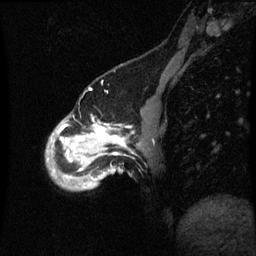
Breast MRI (dynamic contrast-enhanced), one sagittal slice. Position 14 of 60 along the scan axis. Dynamic contrast-enhanced series, image 2 of 3 at this slice position (ordered by acquisition). 1.5 T. TE 4.2 ms, TR 8.9 ms. 2 mm slice thickness. 256 × 256 image matrix, field of view 200 × 200 mm. Female patient, age 49 years. From the clinical record (not read from this slice): setting: breast cancer imaged before/during neoadjuvant chemotherapy; receptor status: HR-positive, HER2-negative.
Structures marked on this image (semi-automatic segmentation, software-assisted and operator-edited):
- analysis volume of interest (the breast-tissue region the enhancement analysis was run in; not a lesion): bounding box (x1, y1, x2, y2) in pixels: (46, 116, 143, 191)
- tumour enhancement mask (voxels above the 70 % enhancement threshold inside the analysis volume of interest): (58, 124, 125, 157)